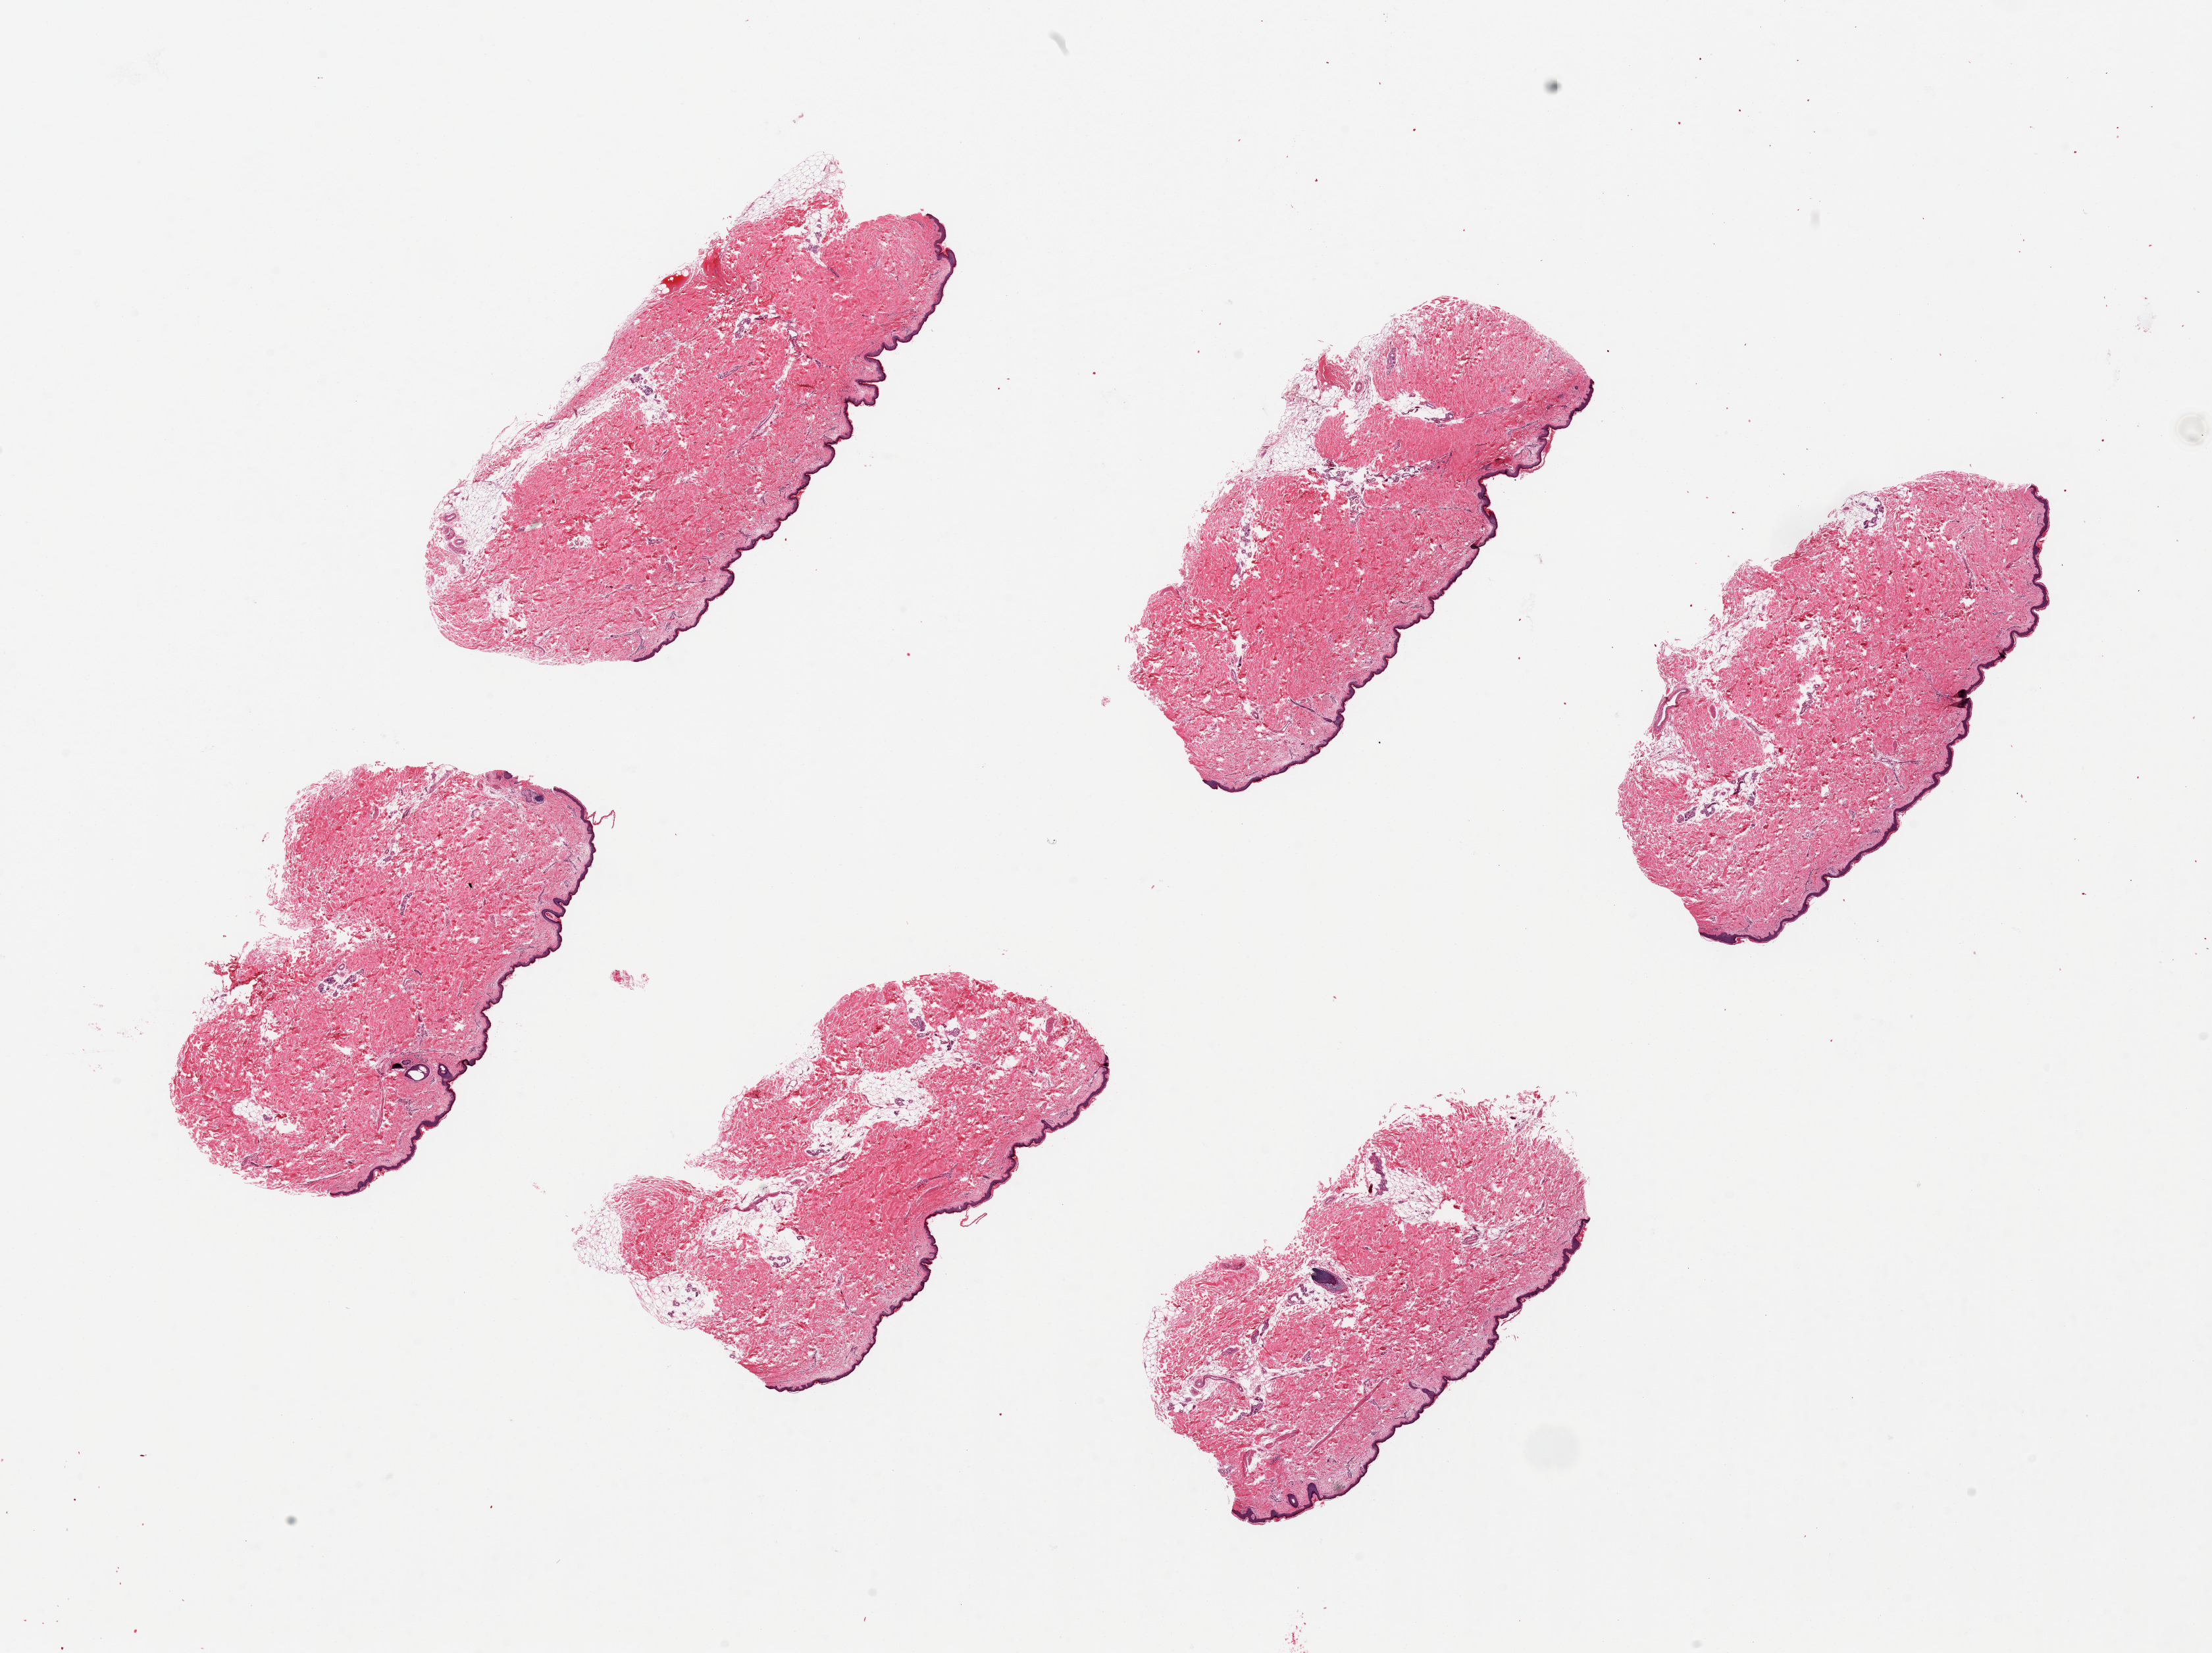
Haematoxylin and eosin whole-slide image, shown as a low-resolution overview of the whole scanned area (about 26.6 x 19.9 mm); PAXgene-fixed paraffin-embedded (PFPE) section; section of skin of lower leg (target tissue); tissue donor sample. Donor sex: male.
- reviewer comment on this tissue sample: 6 pieces, up to 3.4x7.7mm; subcutaneous adipose well trimmed